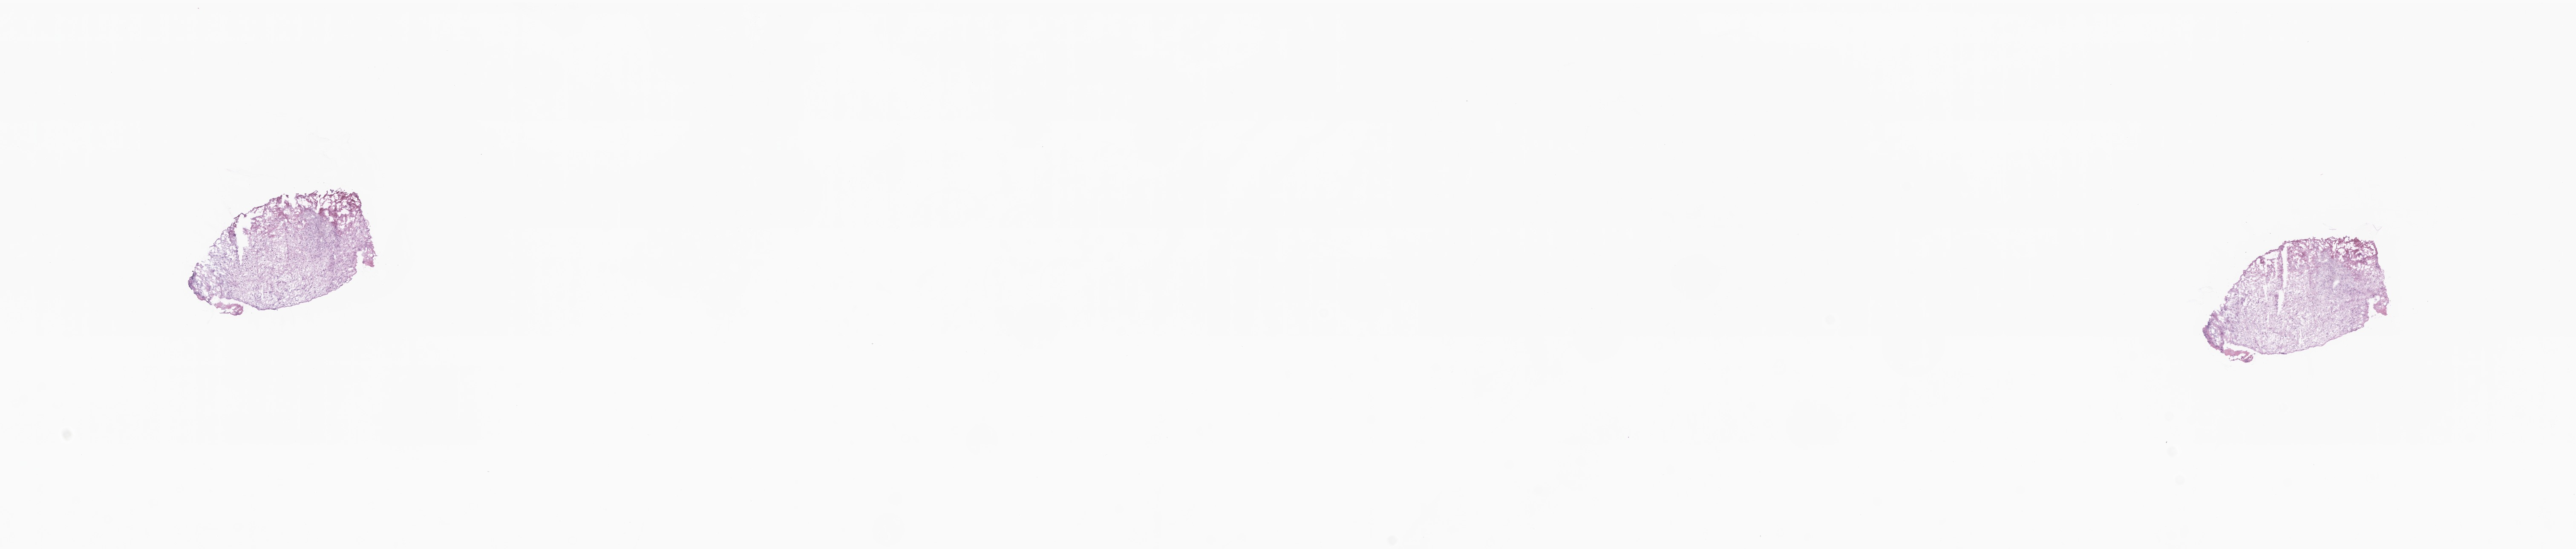
Digitized H&E-stained section — shown as a low-resolution overview of the whole scanned area (about 25.5 x 5.4 mm), frozen section, specimen: primary tumor, anatomic site: breast. Female, age 64 years at initial diagnosis. Composition of this section per pathologist review: tumor cells 25%, tumor nuclei 80%, stromal cells 75%, necrosis 0%, normal cells 0%. Infiltration values recorded for this section: lymphocyte infiltration 0%, monocyte infiltration 0%, neutrophil infiltration 0%.
- section: bottom of the tissue portion
- histologic diagnosis: Lobular carcinoma, NOS